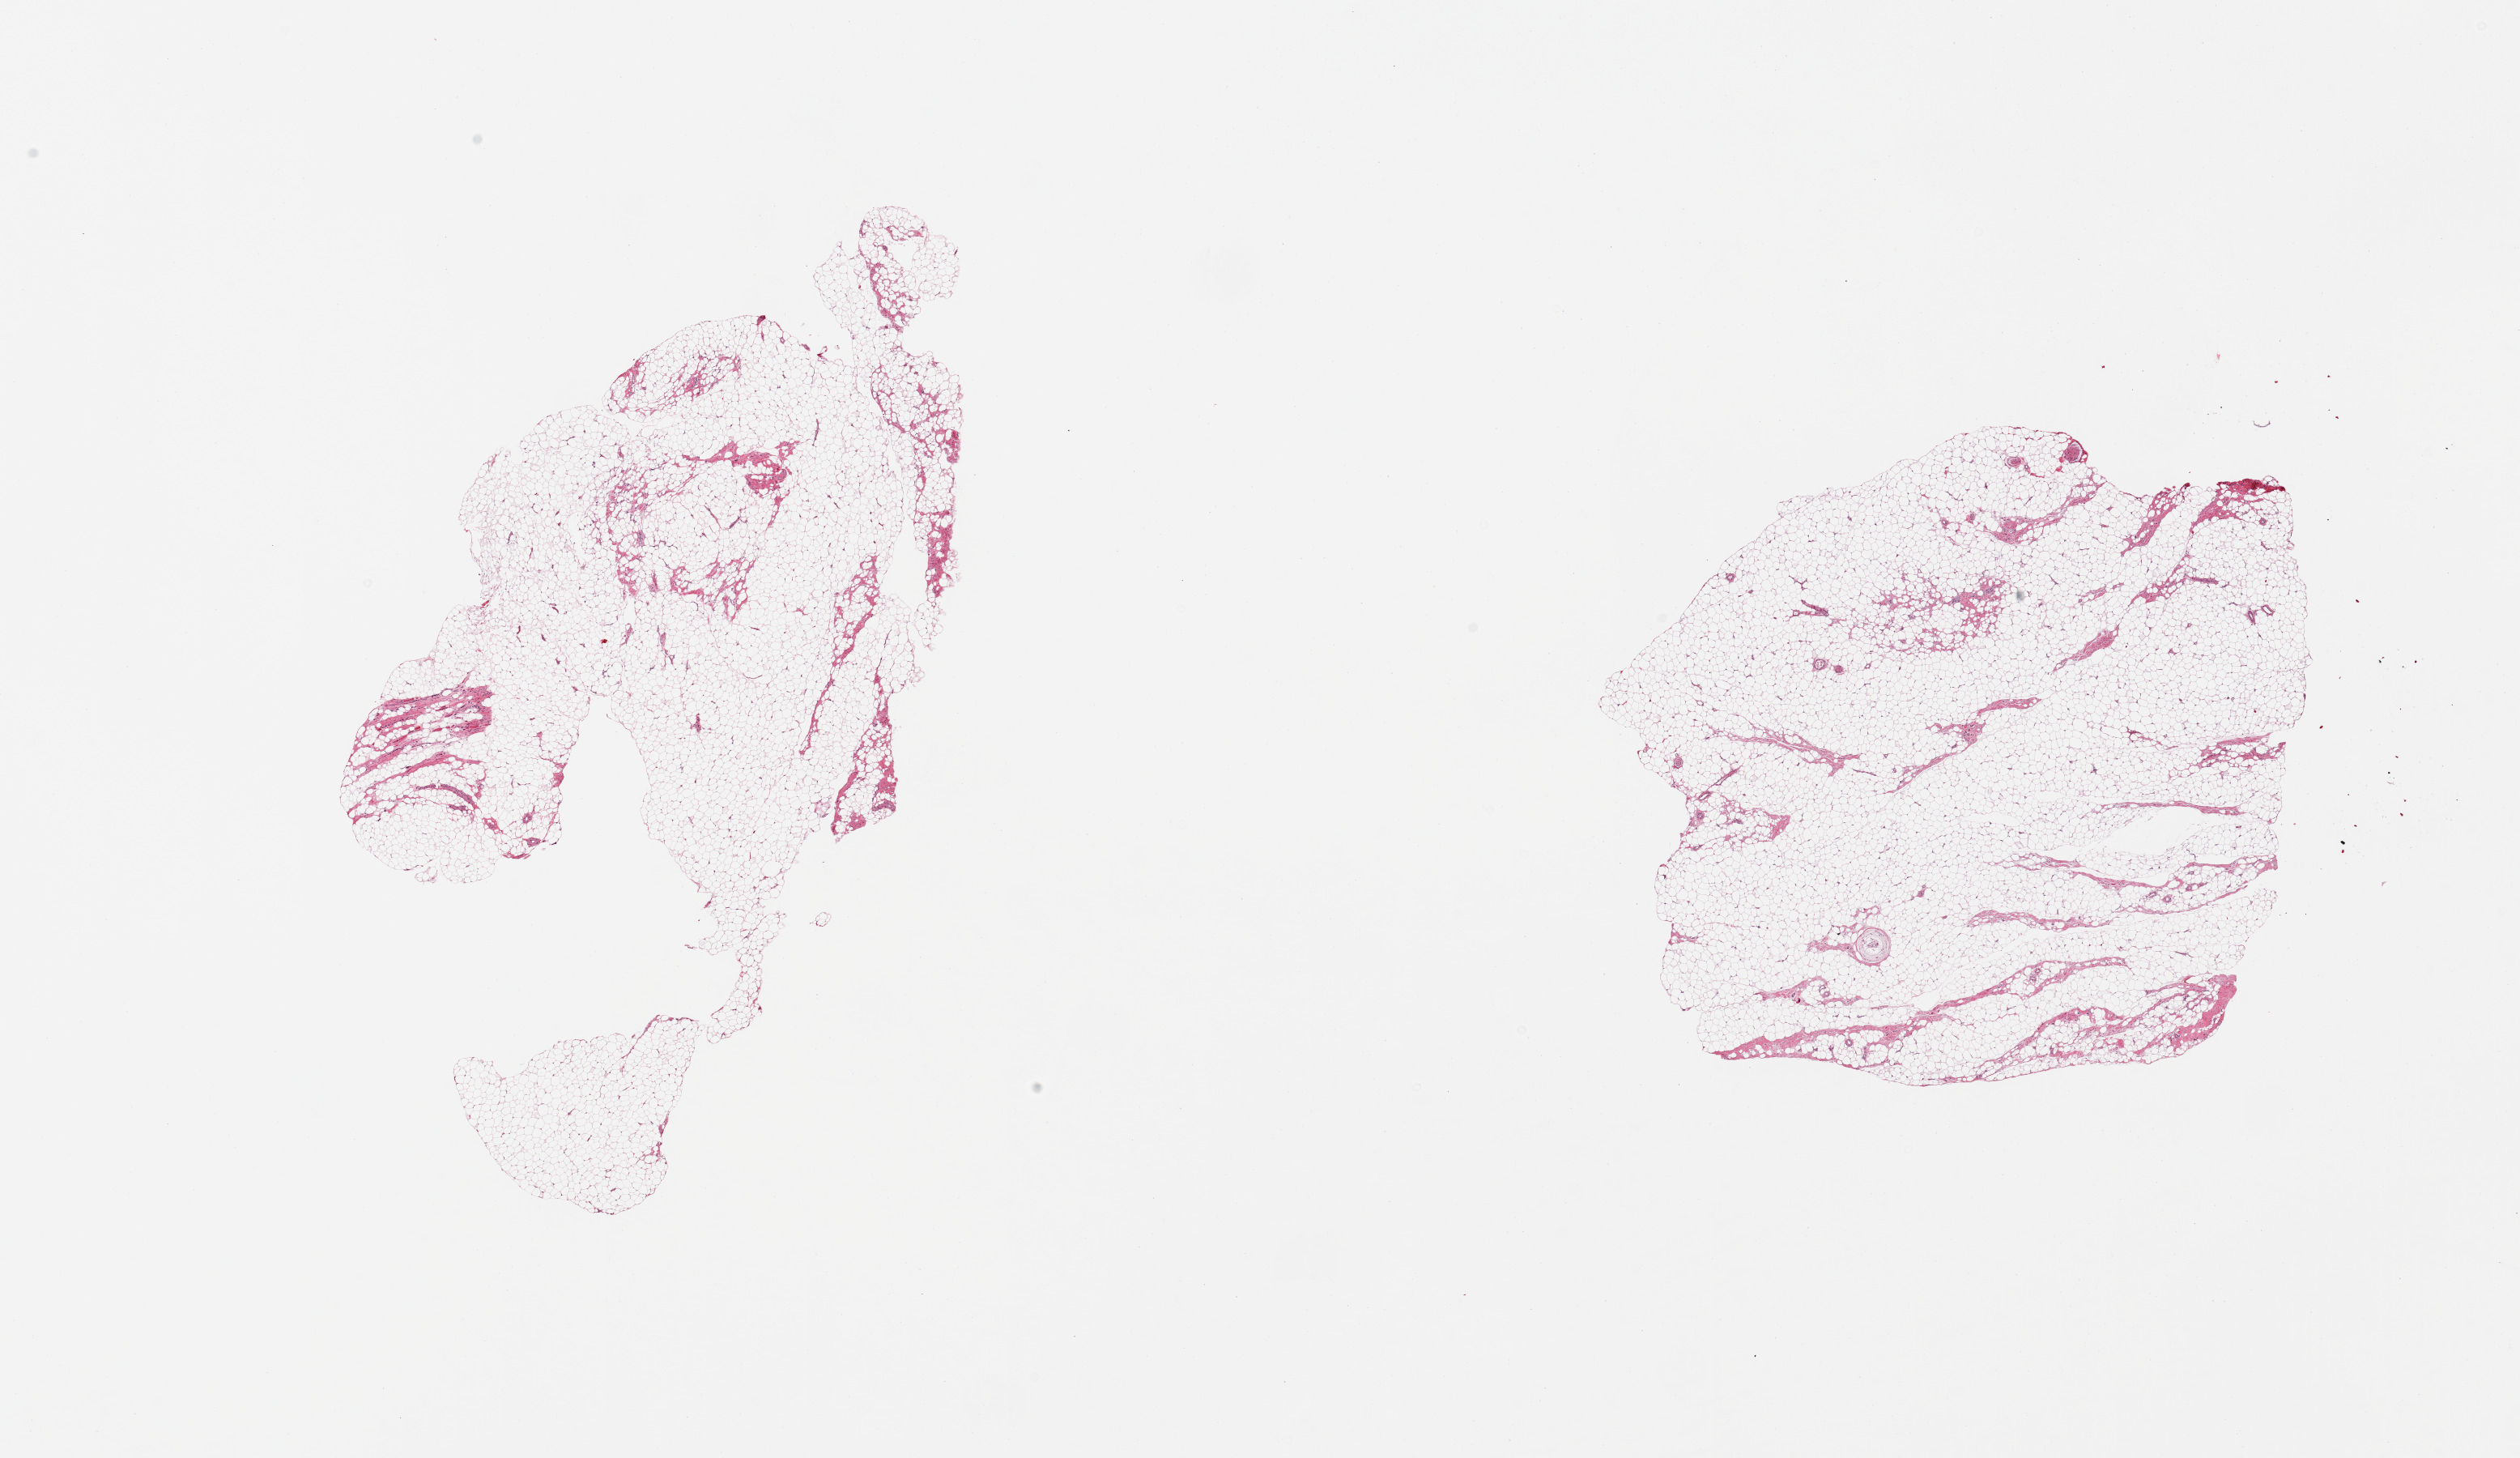
Digitized H&E-stained section, brightfield — shown as a low-resolution overview of the whole scanned area (about 24.6 x 14.2 mm), PAXgene-fixed, paraffin-embedded tissue, sampled site (target tissue): skeletal muscle, tissue donor sample. Male donor.
Review note (as recorded): 2 pieces: 1 has minute focus of atrophic muscle fibers comprising <1% of a largely adipose section; other piece is all fat.